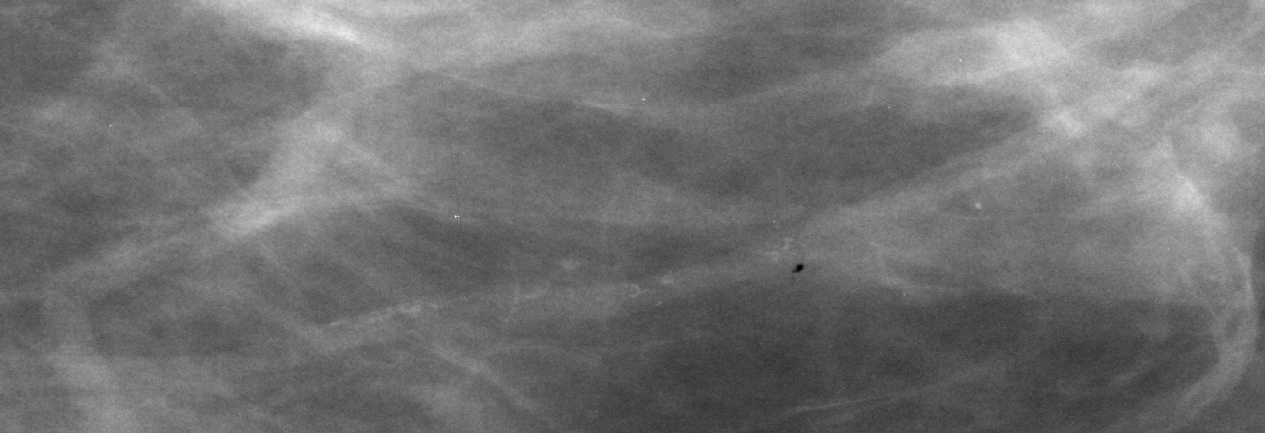
Region of interest cut from a scanned film mammogram (one marked finding), left breast, CC view, BI-RADS breast density category 3 (scale 1–4).
Finding: calcifications, morphology vascular; BI-RADS assessment category 2; benign; no additional work-up was recommended (benign without callback).